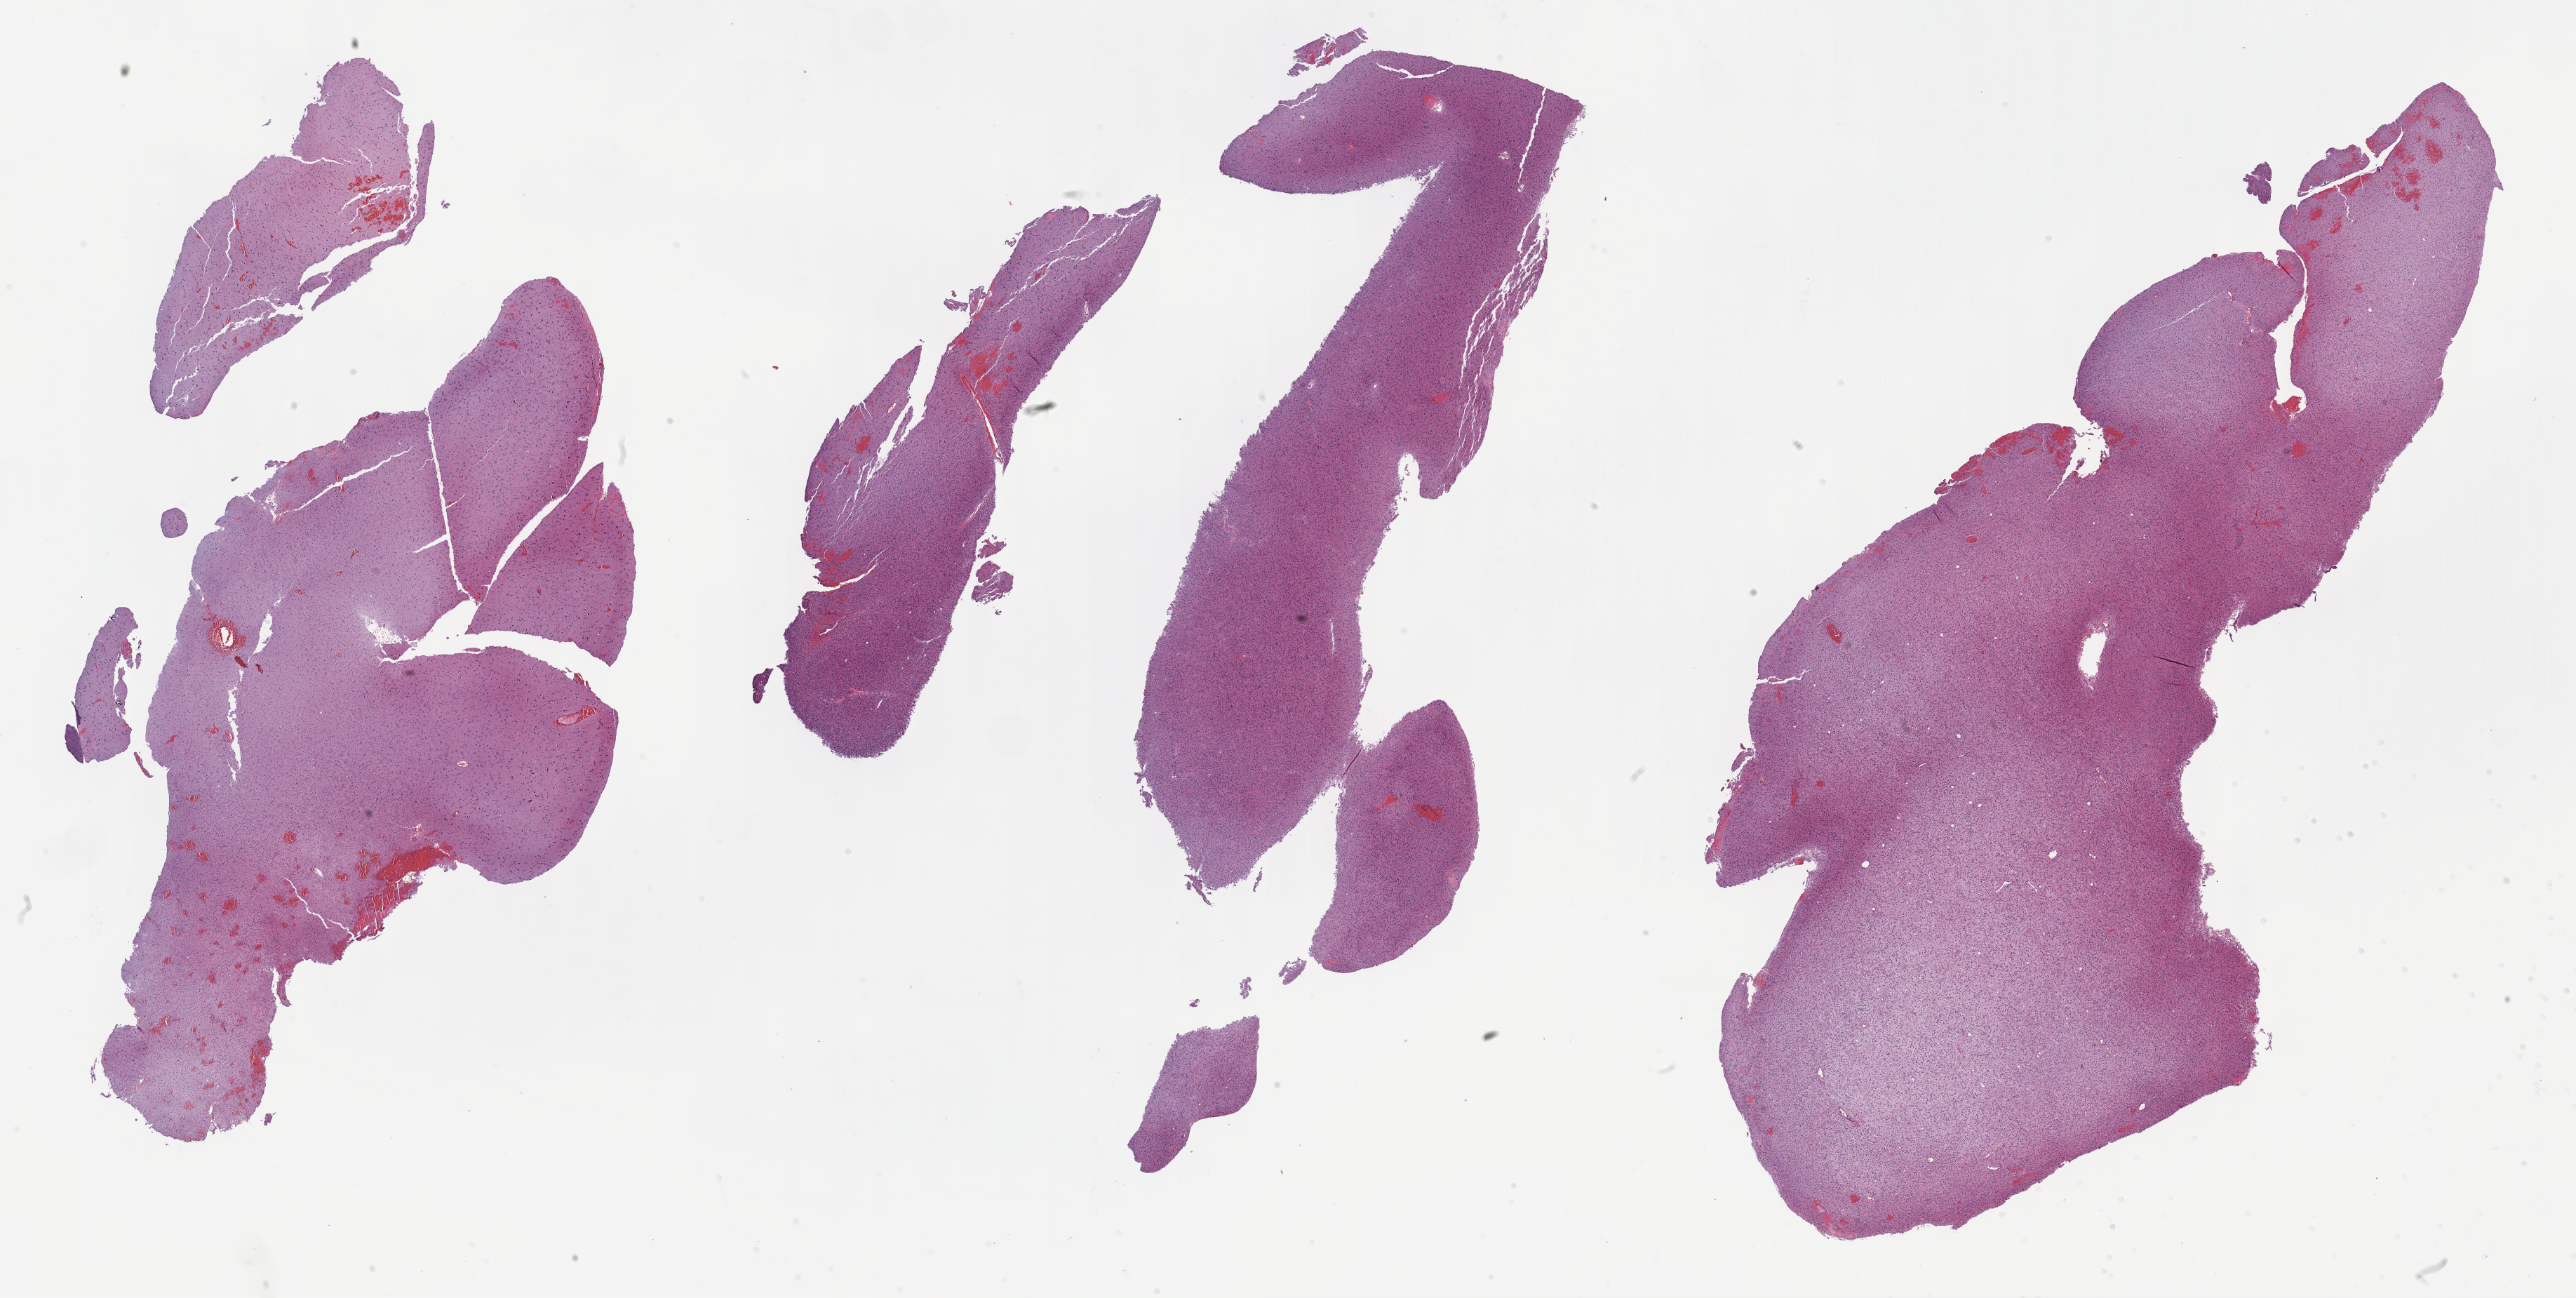
Digitized H&E tissue section (whole slide), a low-resolution overview of the entire scanned area, about 29.7 x 15.0 mm (slide scanned at 40x); FFPE section; brain, primary tumour sample. Male patient; age at initial diagnosis 25 years. Histologic grade: G2 (moderately differentiated).
Diagnosis: Oligodendroglioma, NOS (cerebrum).